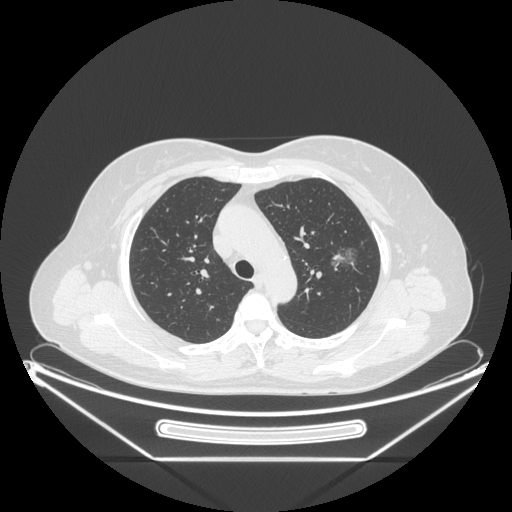
Chest CT, one axial slice; slice 156 of 226 in the series (ordered by position); reconstruction kernel STANDARD; 120 kVp; lung window (W 1500 / L -600 HU); 1.25 mm slice thickness; 512 × 512 image matrix, field of view 447 × 447 mm. Female patient, age 54 years. Case-level facts recorded for this patient, not image findings: clinical TNM (as recorded): T1c N0 M0.
Structures marked on this image (rectangle marked by the reading radiologist):
- lung tumour (recorded histology: adenocarcinoma): bounding box (x1, y1, x2, y2) in pixels: (321, 237, 368, 273)